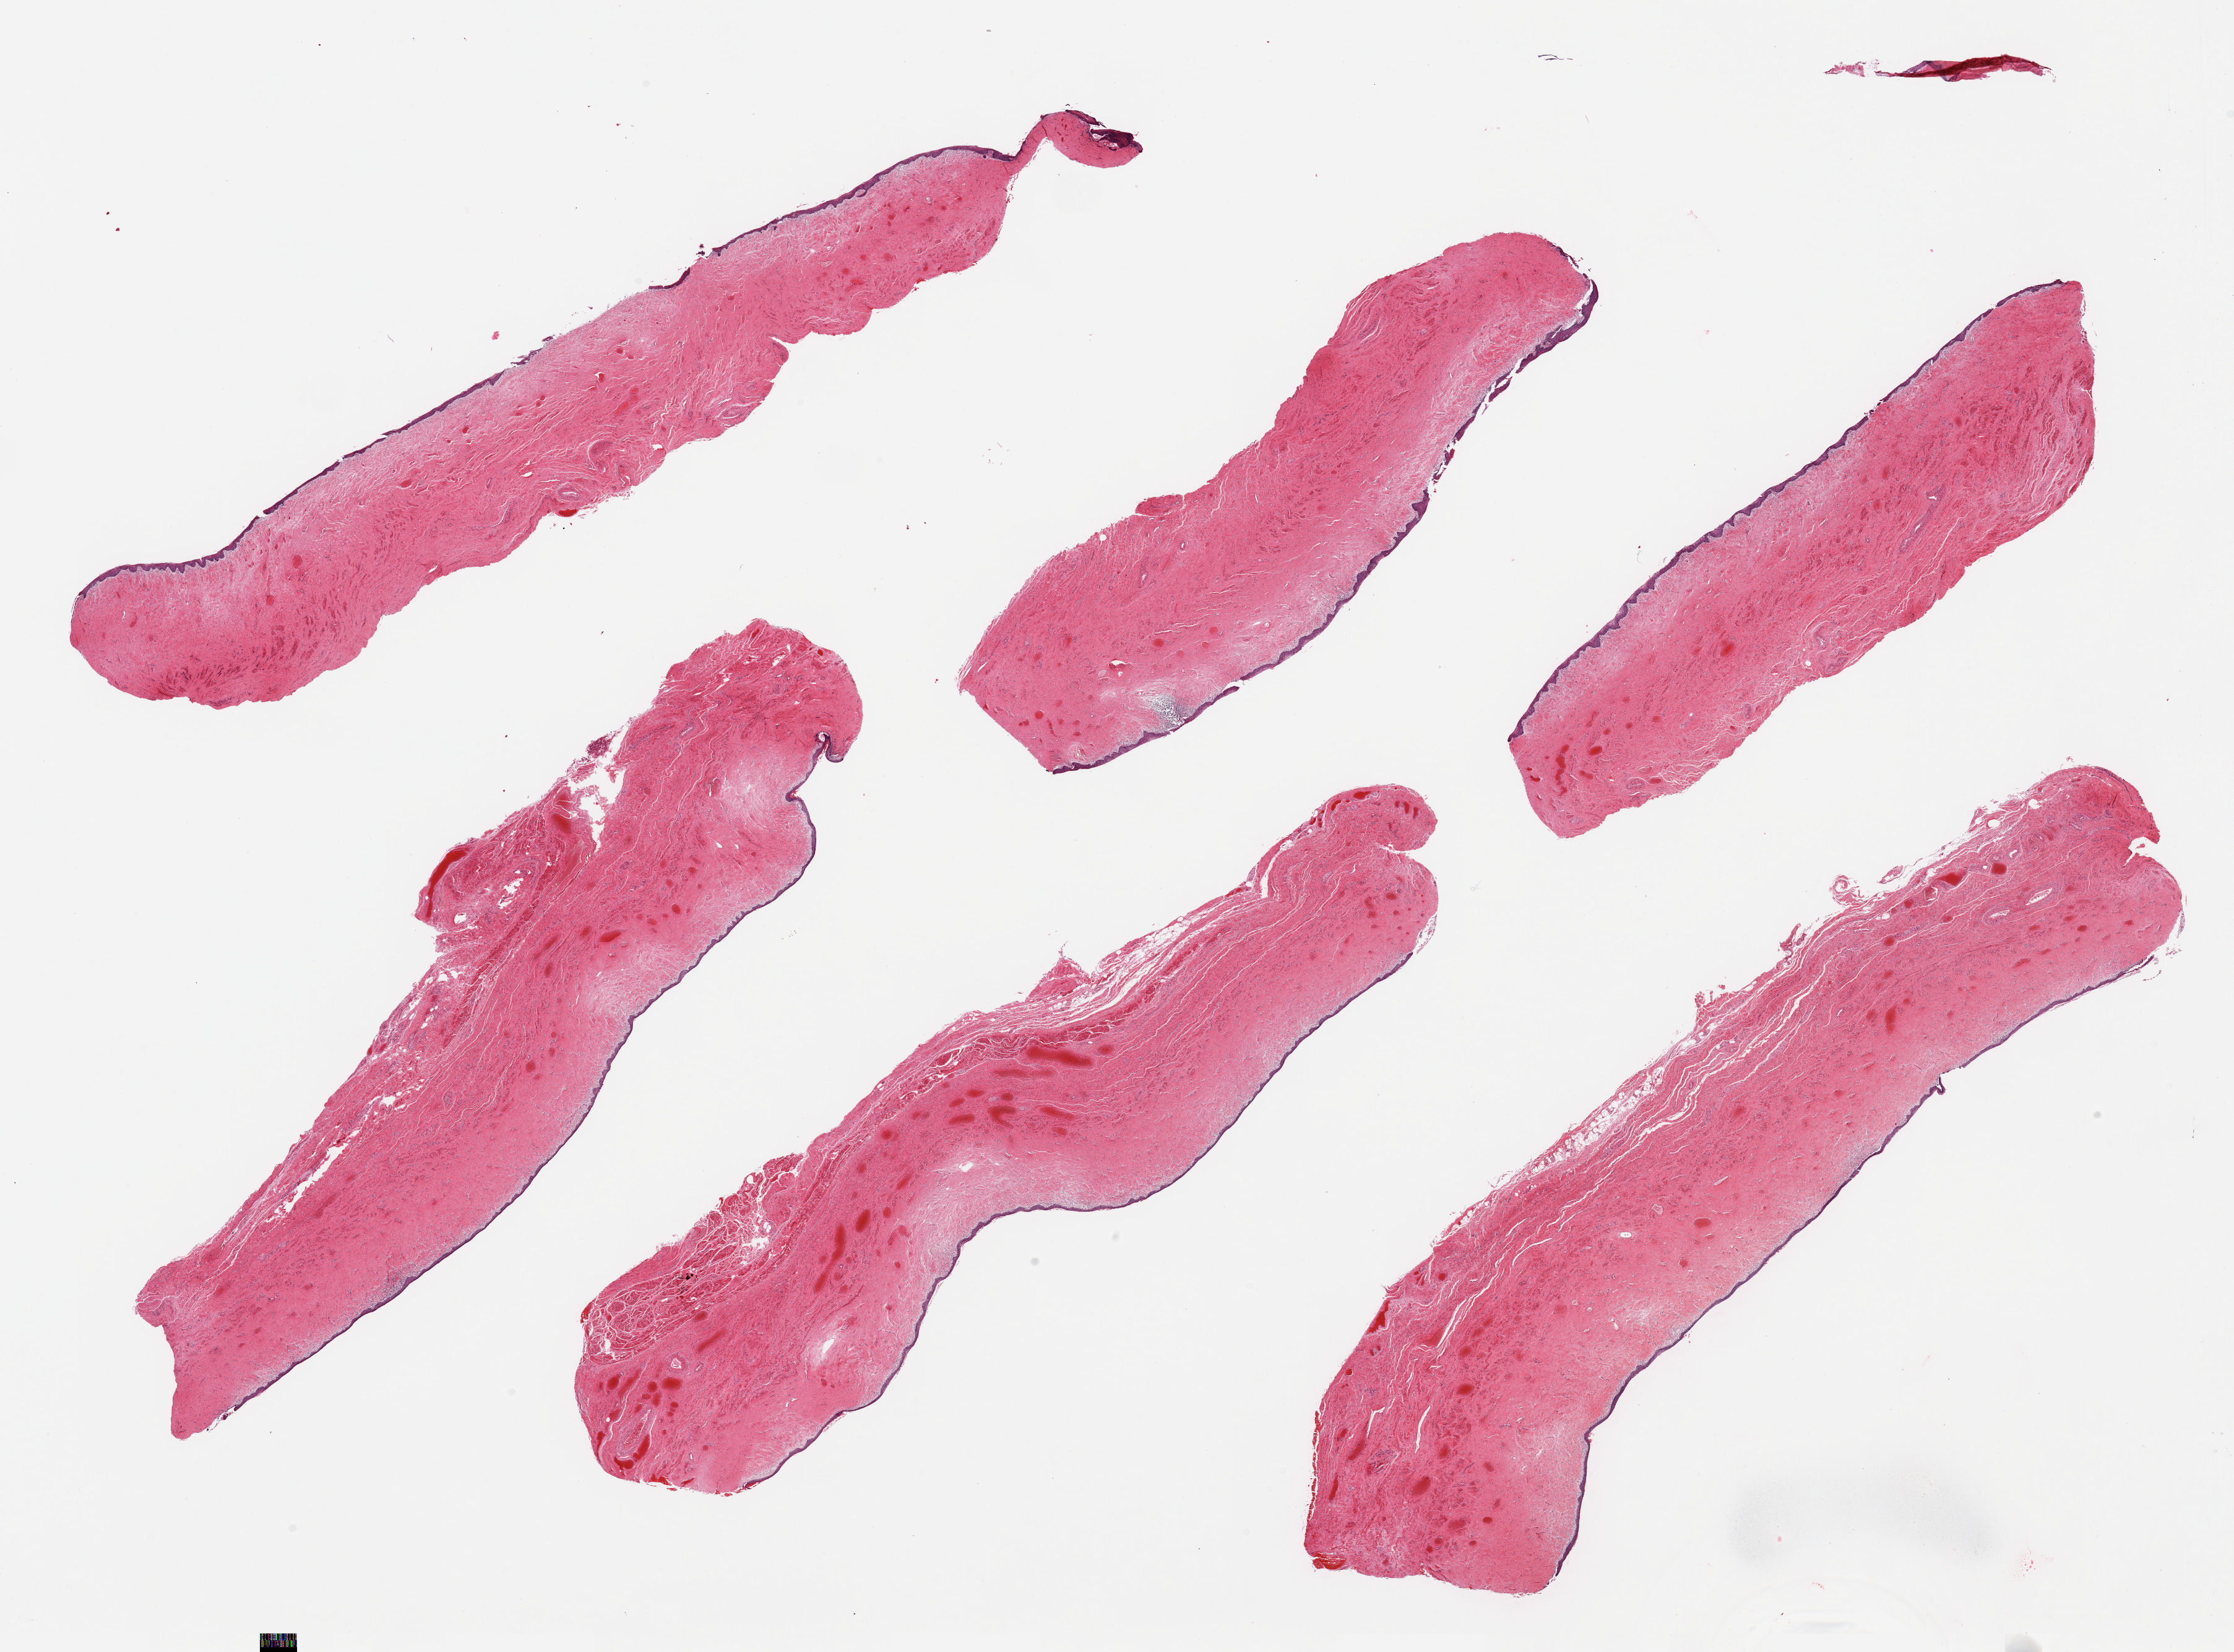
Digitized H&E-stained section, a low-resolution overview of the entire scanned area, about 28.5 x 21.1 mm (acquisition: 20x scan). PAXgene-fixed, paraffin-embedded tissue. Sampled site (target tissue): vagina. Donor tissue sample. Donor sex: female.
Reviewer comment on this tissue sample: 6 pieces, squamous mucosa up to ~0.1mm.